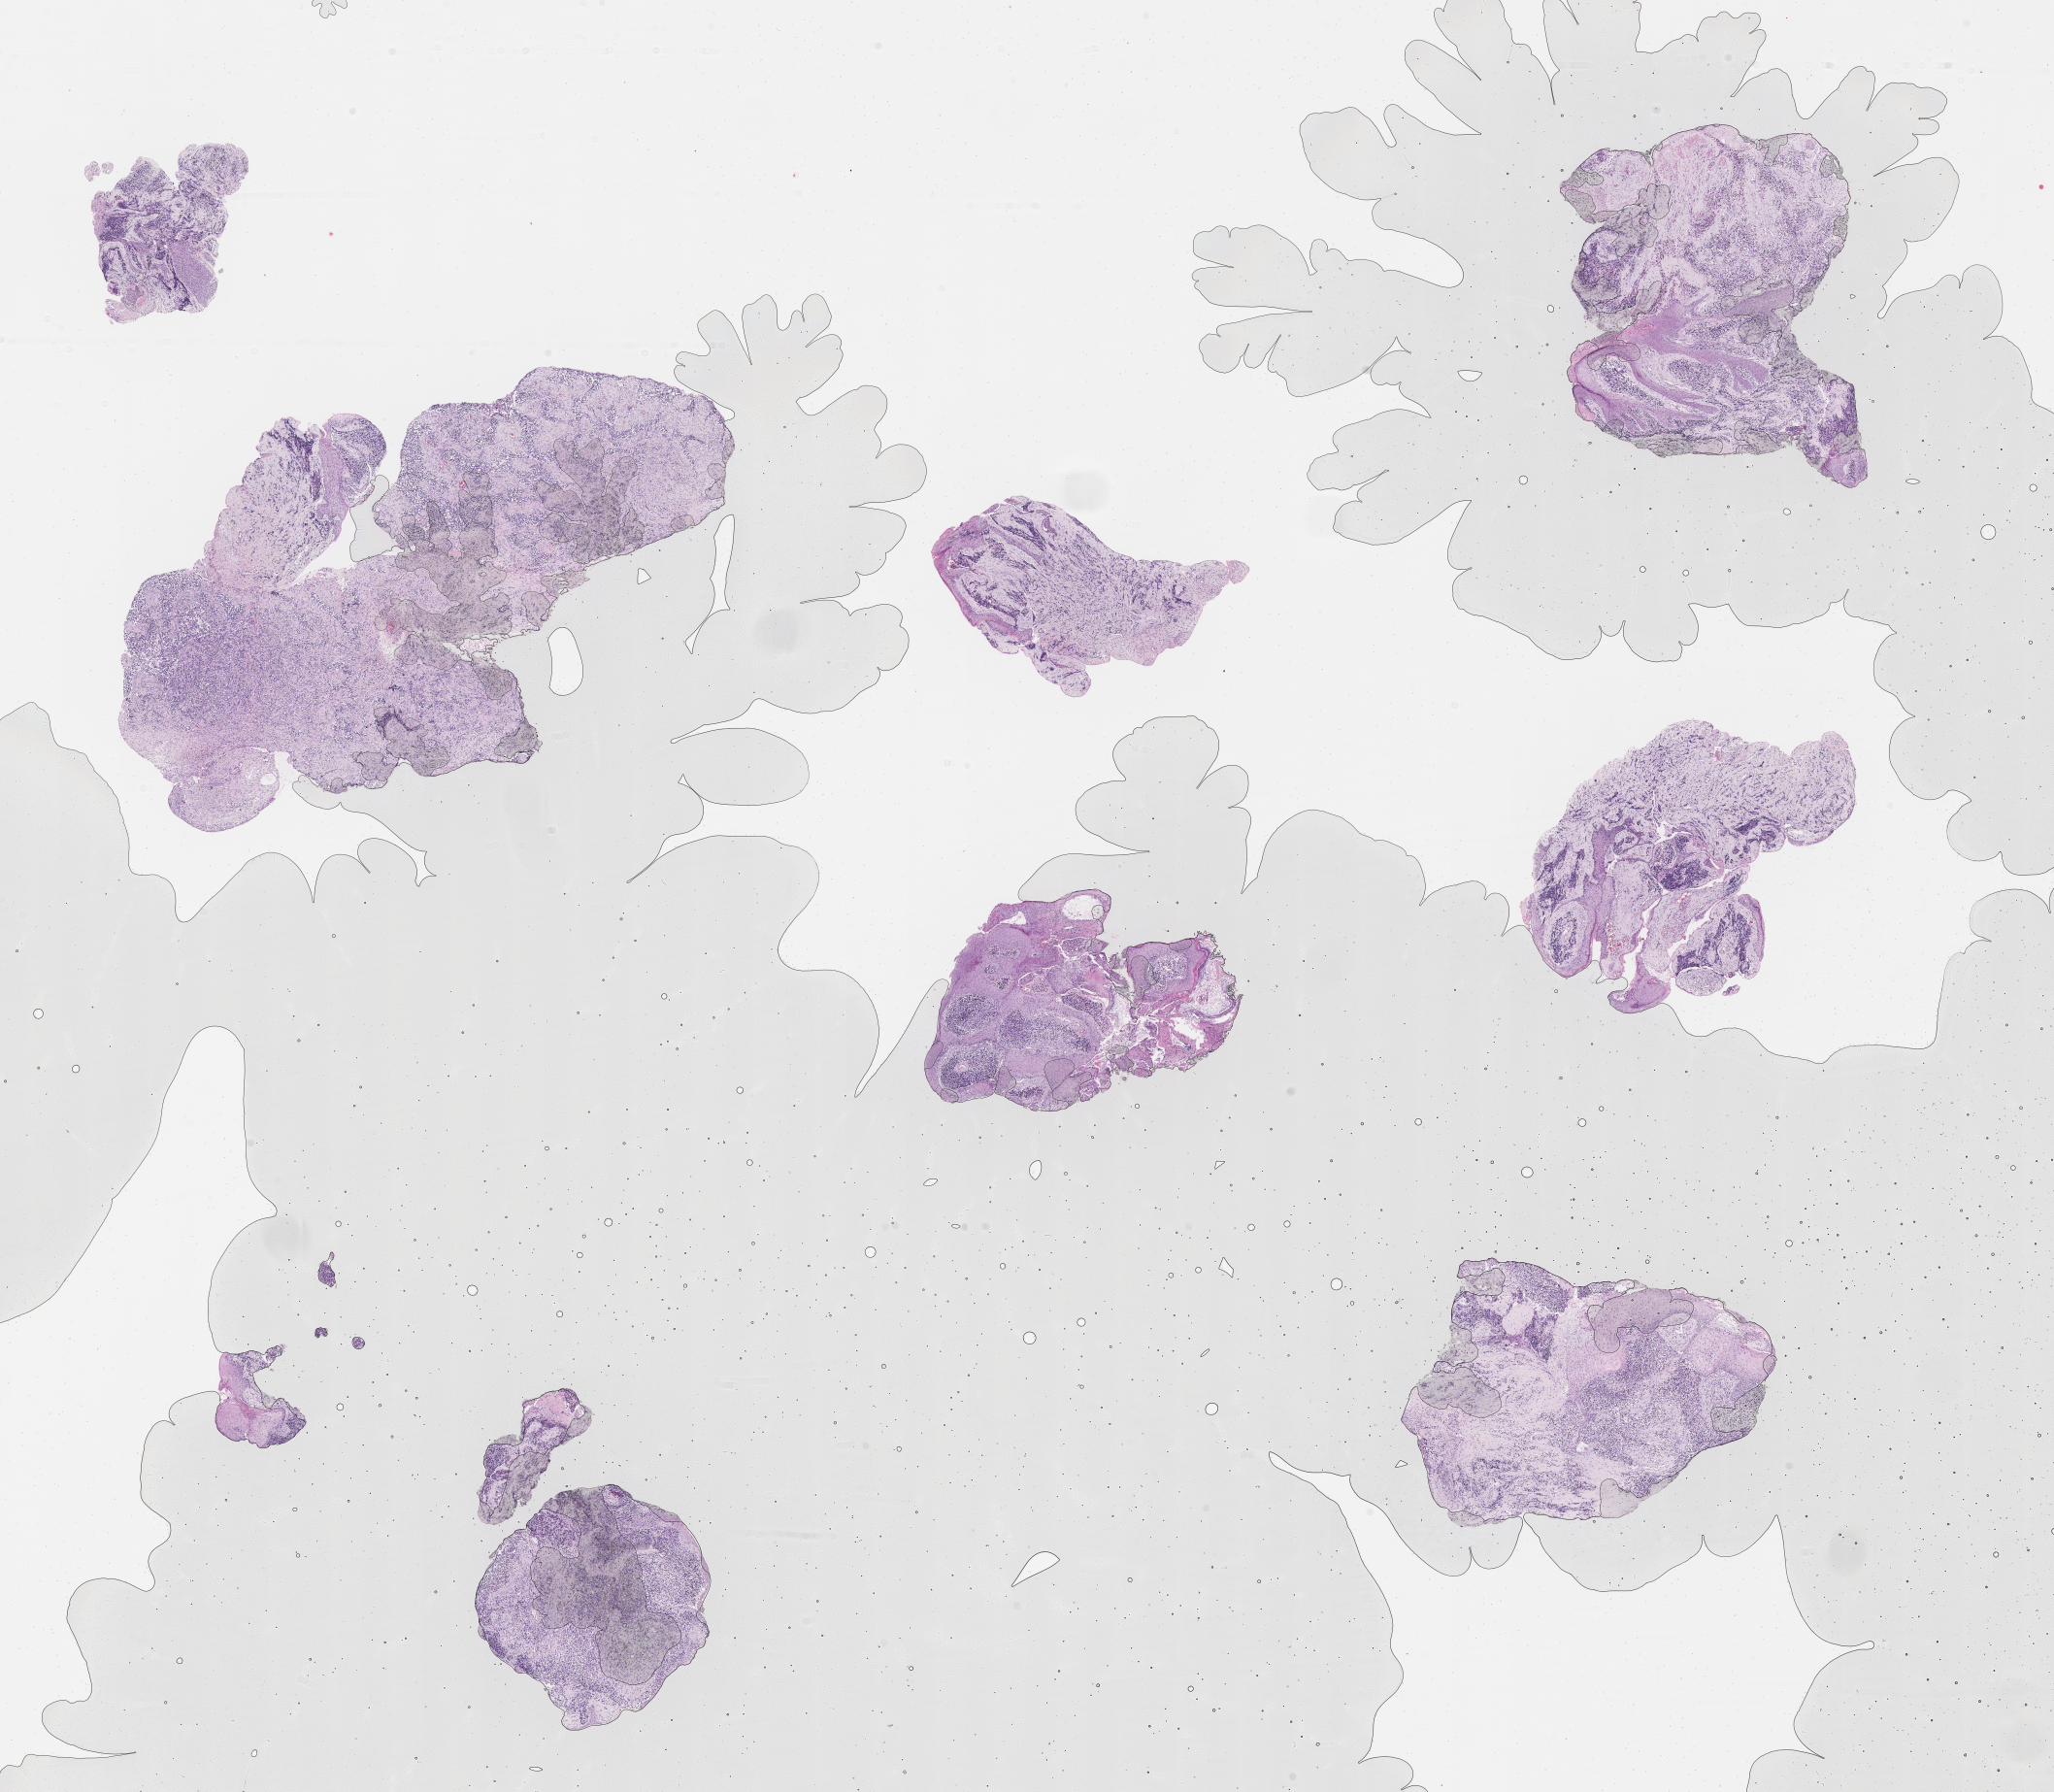
Whole-slide image, haematoxylin and eosin stain of tumor tissue — shown as a low-resolution overview of the whole scanned area (about 17.1 x 14.9 mm), formalin-fixed, paraffin-embedded (FFPE) tissue, sample anatomic site: soft tissue, ear-left. Female patient, age at diagnosis 4.9 years.
• diagnosis: rhabdomyosarcoma; histological classification: embryonal rhabdomyosarcoma
• stage (as recorded): 4
• metastatic status at presentation (as recorded): metastatic (confirmed)